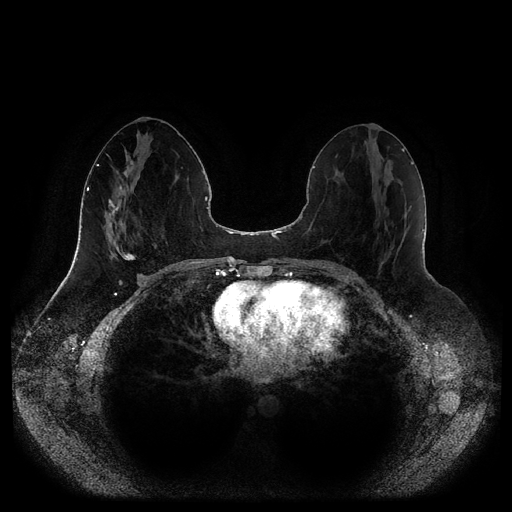
Breast MRI (dynamic contrast-enhanced, multi-phase), one axial slice; dynamic contrast-enhanced series, time point 2 of 5 at this slice position (early post-contrast); 1.5 T; TE 2.5 ms, TR 5.2 ms; 2 mm slice thickness; 512 × 512 image matrix. Patient: female, 44 years.
Annotated regions visible in this slice (semi-automatic segmentation, software-assisted and operator-edited):
- breast lesion (labelled 'tumour' in the annotation; benign lesions carry a separate 'benign' label): bounding box [x1, y1, x2, y2] px = [122, 252, 136, 262]